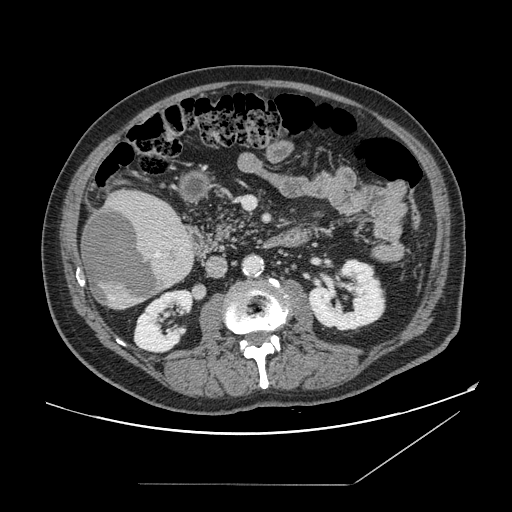
Contrast-enhanced abdominal CT, one axial slice. Position 58 of 166 along the scan axis. 120 kVp. Intravenous contrast given. Soft-tissue window (W 400 / L 40 HU). 512 × 512 image matrix. Male patient, age 80 years. From the clinical record (not read from this slice): diagnosis: colorectal cancer liver metastases, imaged before liver resection; multiple liver metastases: no; largest metastasis: 2.2 cm; disease in both lobes: no.
Outlined on this slice (outlined manually by an expert reader):
- liver: bounding box [x1, y1, x2, y2] px = [81, 190, 195, 309]
- planned liver remnant (the part of the liver to remain after resection): [139, 194, 164, 206]
- liver metastasis: [84, 208, 166, 303]